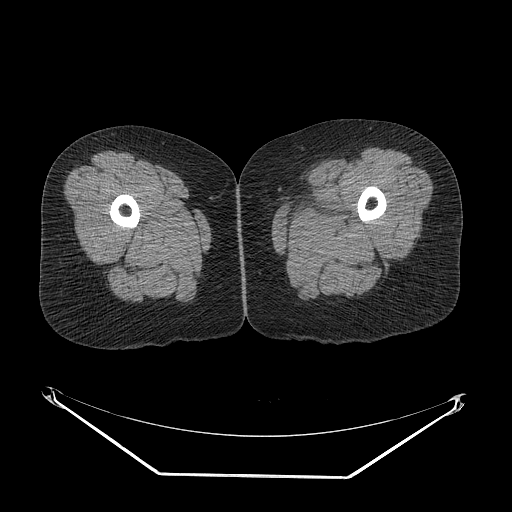
CT of an extremity soft-tissue mass (from a PET/CT study), one axial slice; position 6 of 267 along the scan axis; reconstruction kernel STANDARD; 140 kVp; soft-tissue window (W 400 / L 40 HU); 3.75 mm slice thickness; 512 × 512 image matrix, field of view 500 × 500 mm. Female patient. Case-level facts recorded for this patient, not image findings: histological type: myxofibrosarcoma; grade: intermediate; site of the primary tumour: left thigh.
Structures marked on this image (expert contour drawn on MRI and transferred to this co-registered scan by the dataset authors):
- gross tumour volume including surrounding oedema: bounding box <285,196,348,234> (left, top, right, bottom; pixels)